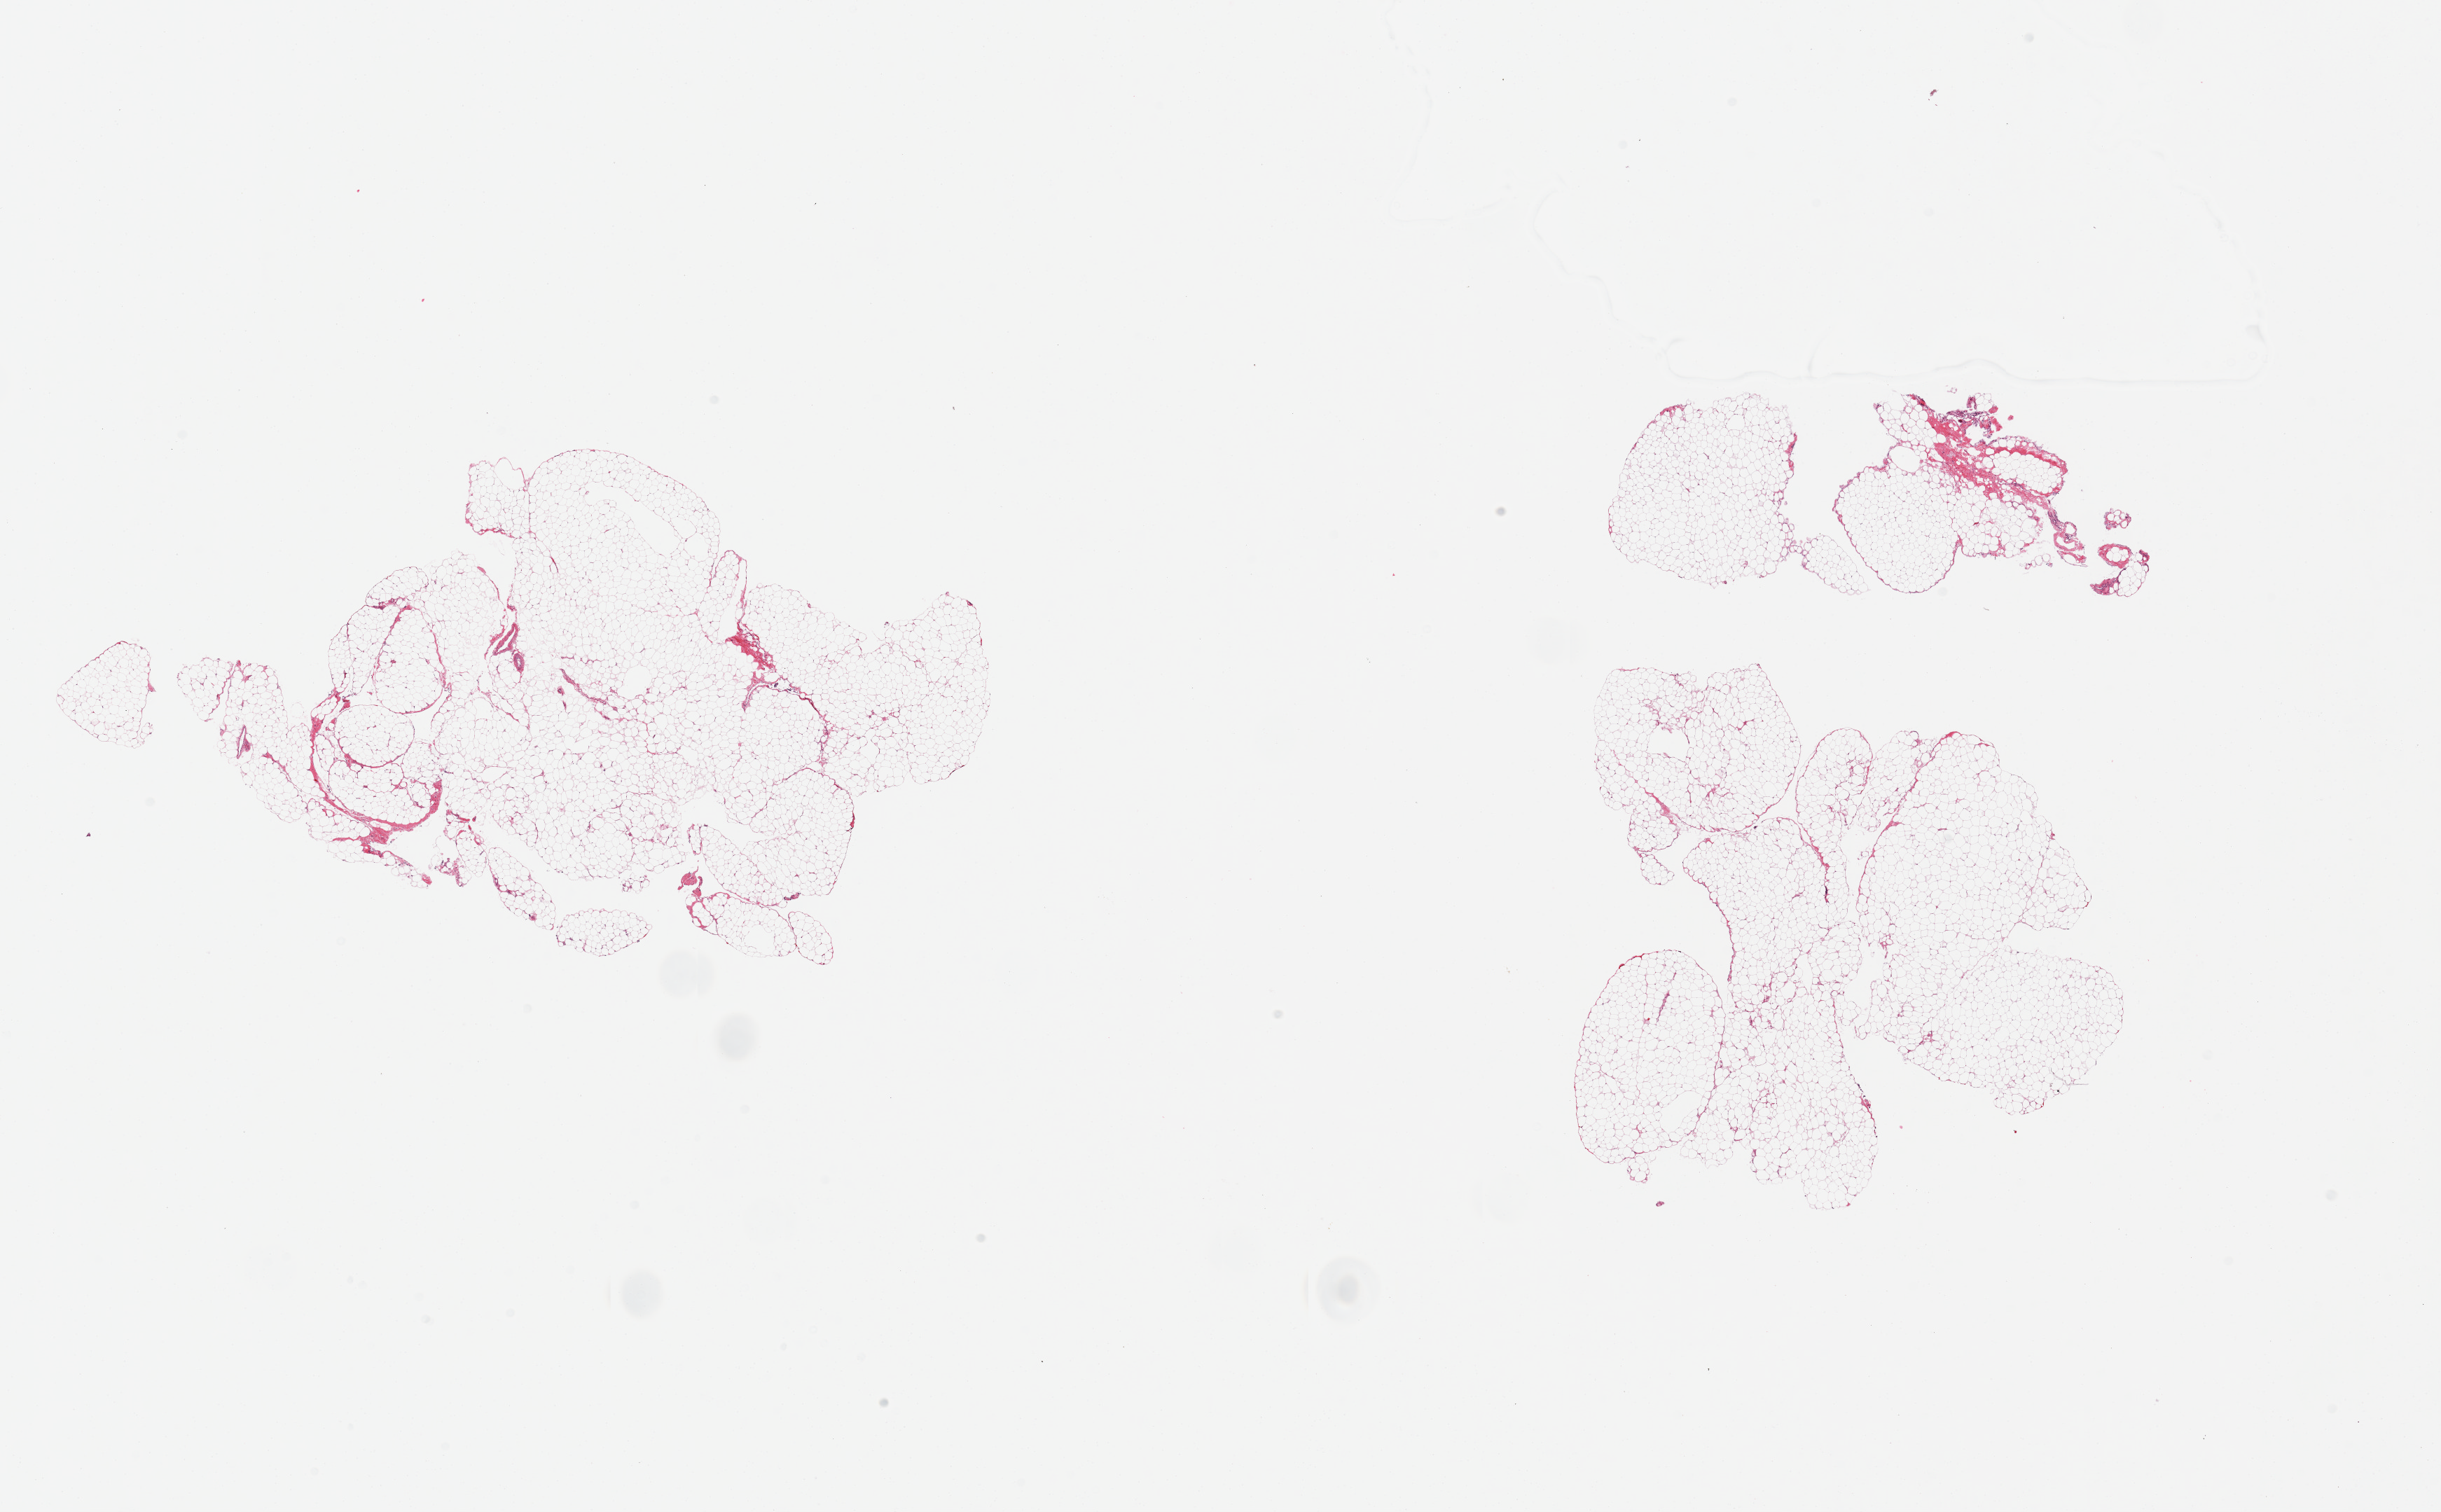
Digitized haematoxylin and eosin-stained section — whole scanned area (about 27.6 x 17.1 mm) shown as a low-resolution overview, PAXgene-fixed paraffin-embedded (PFPE) section, section of omentum (target tissue), tissue donor sample. Donor: male.
Review note (as recorded): 2 pieces.